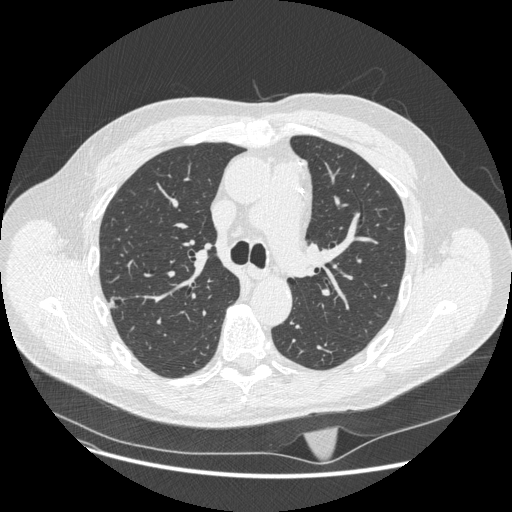
Low-dose screening chest CT, axial slice. Second annual screen. Lung window (W 1500 / L -600 HU). 120 kVp. Slice 77 of 247 in the series. Male, age 62 years at enrolment. Current smoker at enrolment.
Expert-annotated lung lesion, bounding box (x1, y1, x2, y2) in pixels: (97, 289, 130, 317). The exam's reader record, not a measurement of the box and not confirmed to be the same lesion: non-calcified nodule or mass ≥4 mm, right upper lobe, 11 × 7 mm, smooth margins, pre-existing on the prior screen: yes. Official screen result: positive, change unspecified: nodule(s) >= 4 mm or enlarging nodule(s), mass(es), or other non-specific abnormalities suspicious for lung cancer. Lung cancer was diagnosed 482 days after this screen: adenocarcinoma, NOS, right upper lobe, moderately differentiated (G2), stage IA (AJCC 6th edition), 12 mm at pathology.